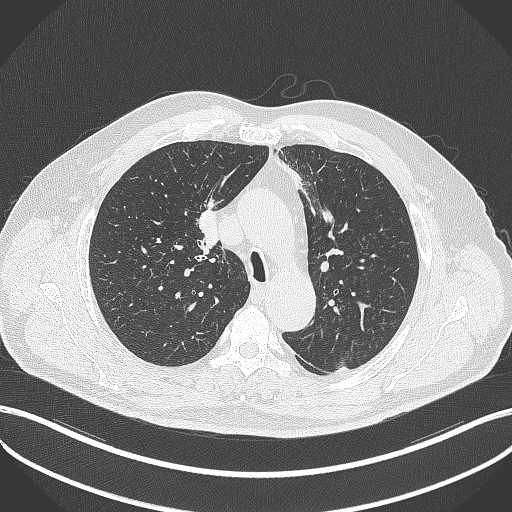
Chest CT, one axial slice. Position 272 of 411 along the scan axis. Reconstruction kernel B70f. 120 kVp. Lung window (W 1500 / L -600 HU). 512 × 512 image matrix. Male patient, age 60 years. Case-level facts recorded for this patient, not image findings: clinical TNM (as recorded): T1b N1 M0.
Annotated regions visible in this slice (rectangle marked by the reading radiologist):
- lung tumour (recorded histology: squamous cell carcinoma): bounding box <194,203,221,251> (left, top, right, bottom; pixels)